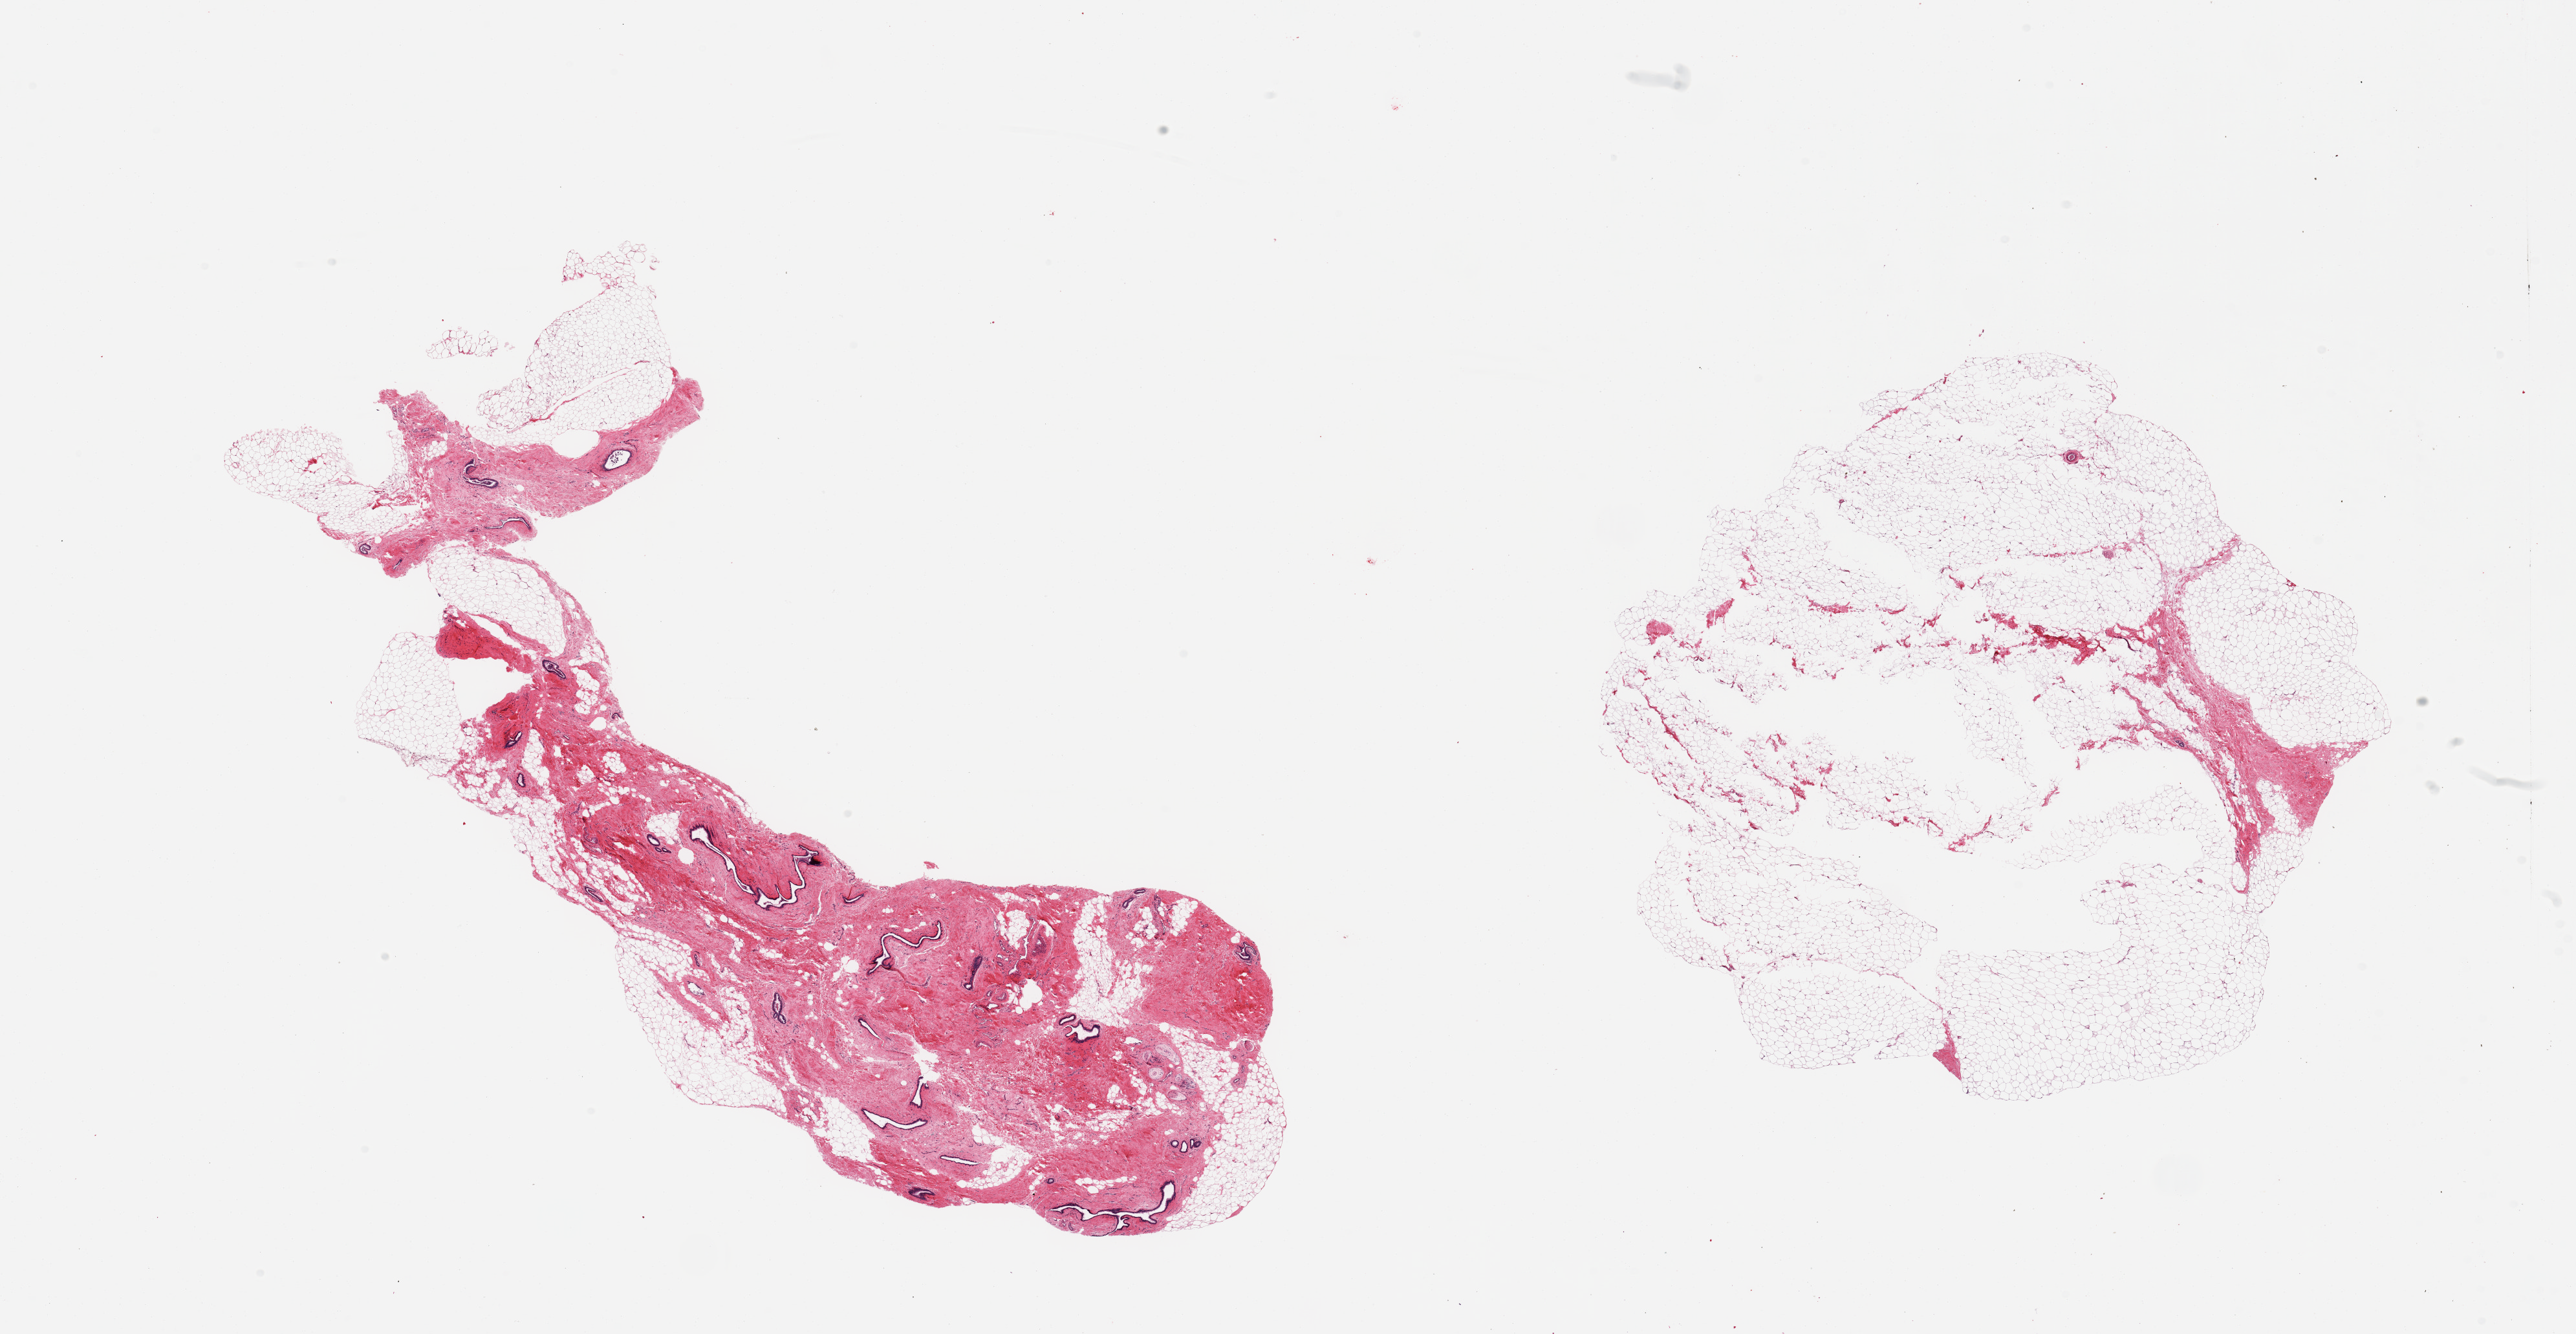
Whole-slide image, H&E stain, a low-resolution overview of the entire scanned area, about 31.5 x 16.3 mm, PAXgene-fixed paraffin-embedded (PFPE) section, sampled site (target tissue): breast, tissue donor sample. Male donor.
Reviewer comment on this tissue sample: 2 pieces, gynecomastoid stromal and focal ductal hyperplasia; rep ductal elements.